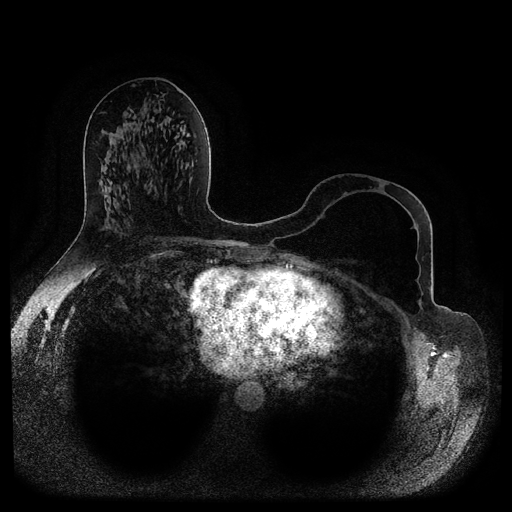
Breast MRI (dynamic contrast-enhanced, multi-phase), one axial slice. Slice 47 of 116 in the series (ordered by position). Dynamic contrast-enhanced series, time point 2 of 5 at this slice position (early post-contrast). 1.5 T. TE 2.6 ms, TR 5.2 ms. 2 mm slice thickness. 512 × 512 image matrix, field of view 380 × 380 mm. Female patient, age 56 years.
Annotated regions visible in this slice (semi-automatically segmented with operator editing):
- breast lesion (labelled benign in the annotation): bounding box (x1, y1, x2, y2) in pixels: (157, 124, 161, 127)